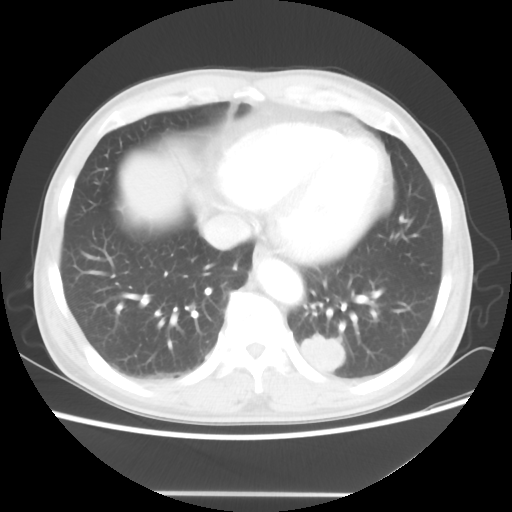
Chest CT, one axial slice. Position 17 of 60 along the scan axis. Reconstruction kernel STANDARD. 100 kVp. Lung window (W 1500 / L -600 HU). 512 × 512 image matrix, field of view 360 × 360 mm. Male patient, age 55 years. From the clinical record (not read from this slice): clinical TNM (as recorded): T1c N3 M0; histopathological grade: G3.
Structures marked on this image (bounding box drawn by a radiologist):
- lung tumour (recorded histology: small cell carcinoma): bounding box (x1, y1, x2, y2) in pixels: (299, 330, 345, 379)